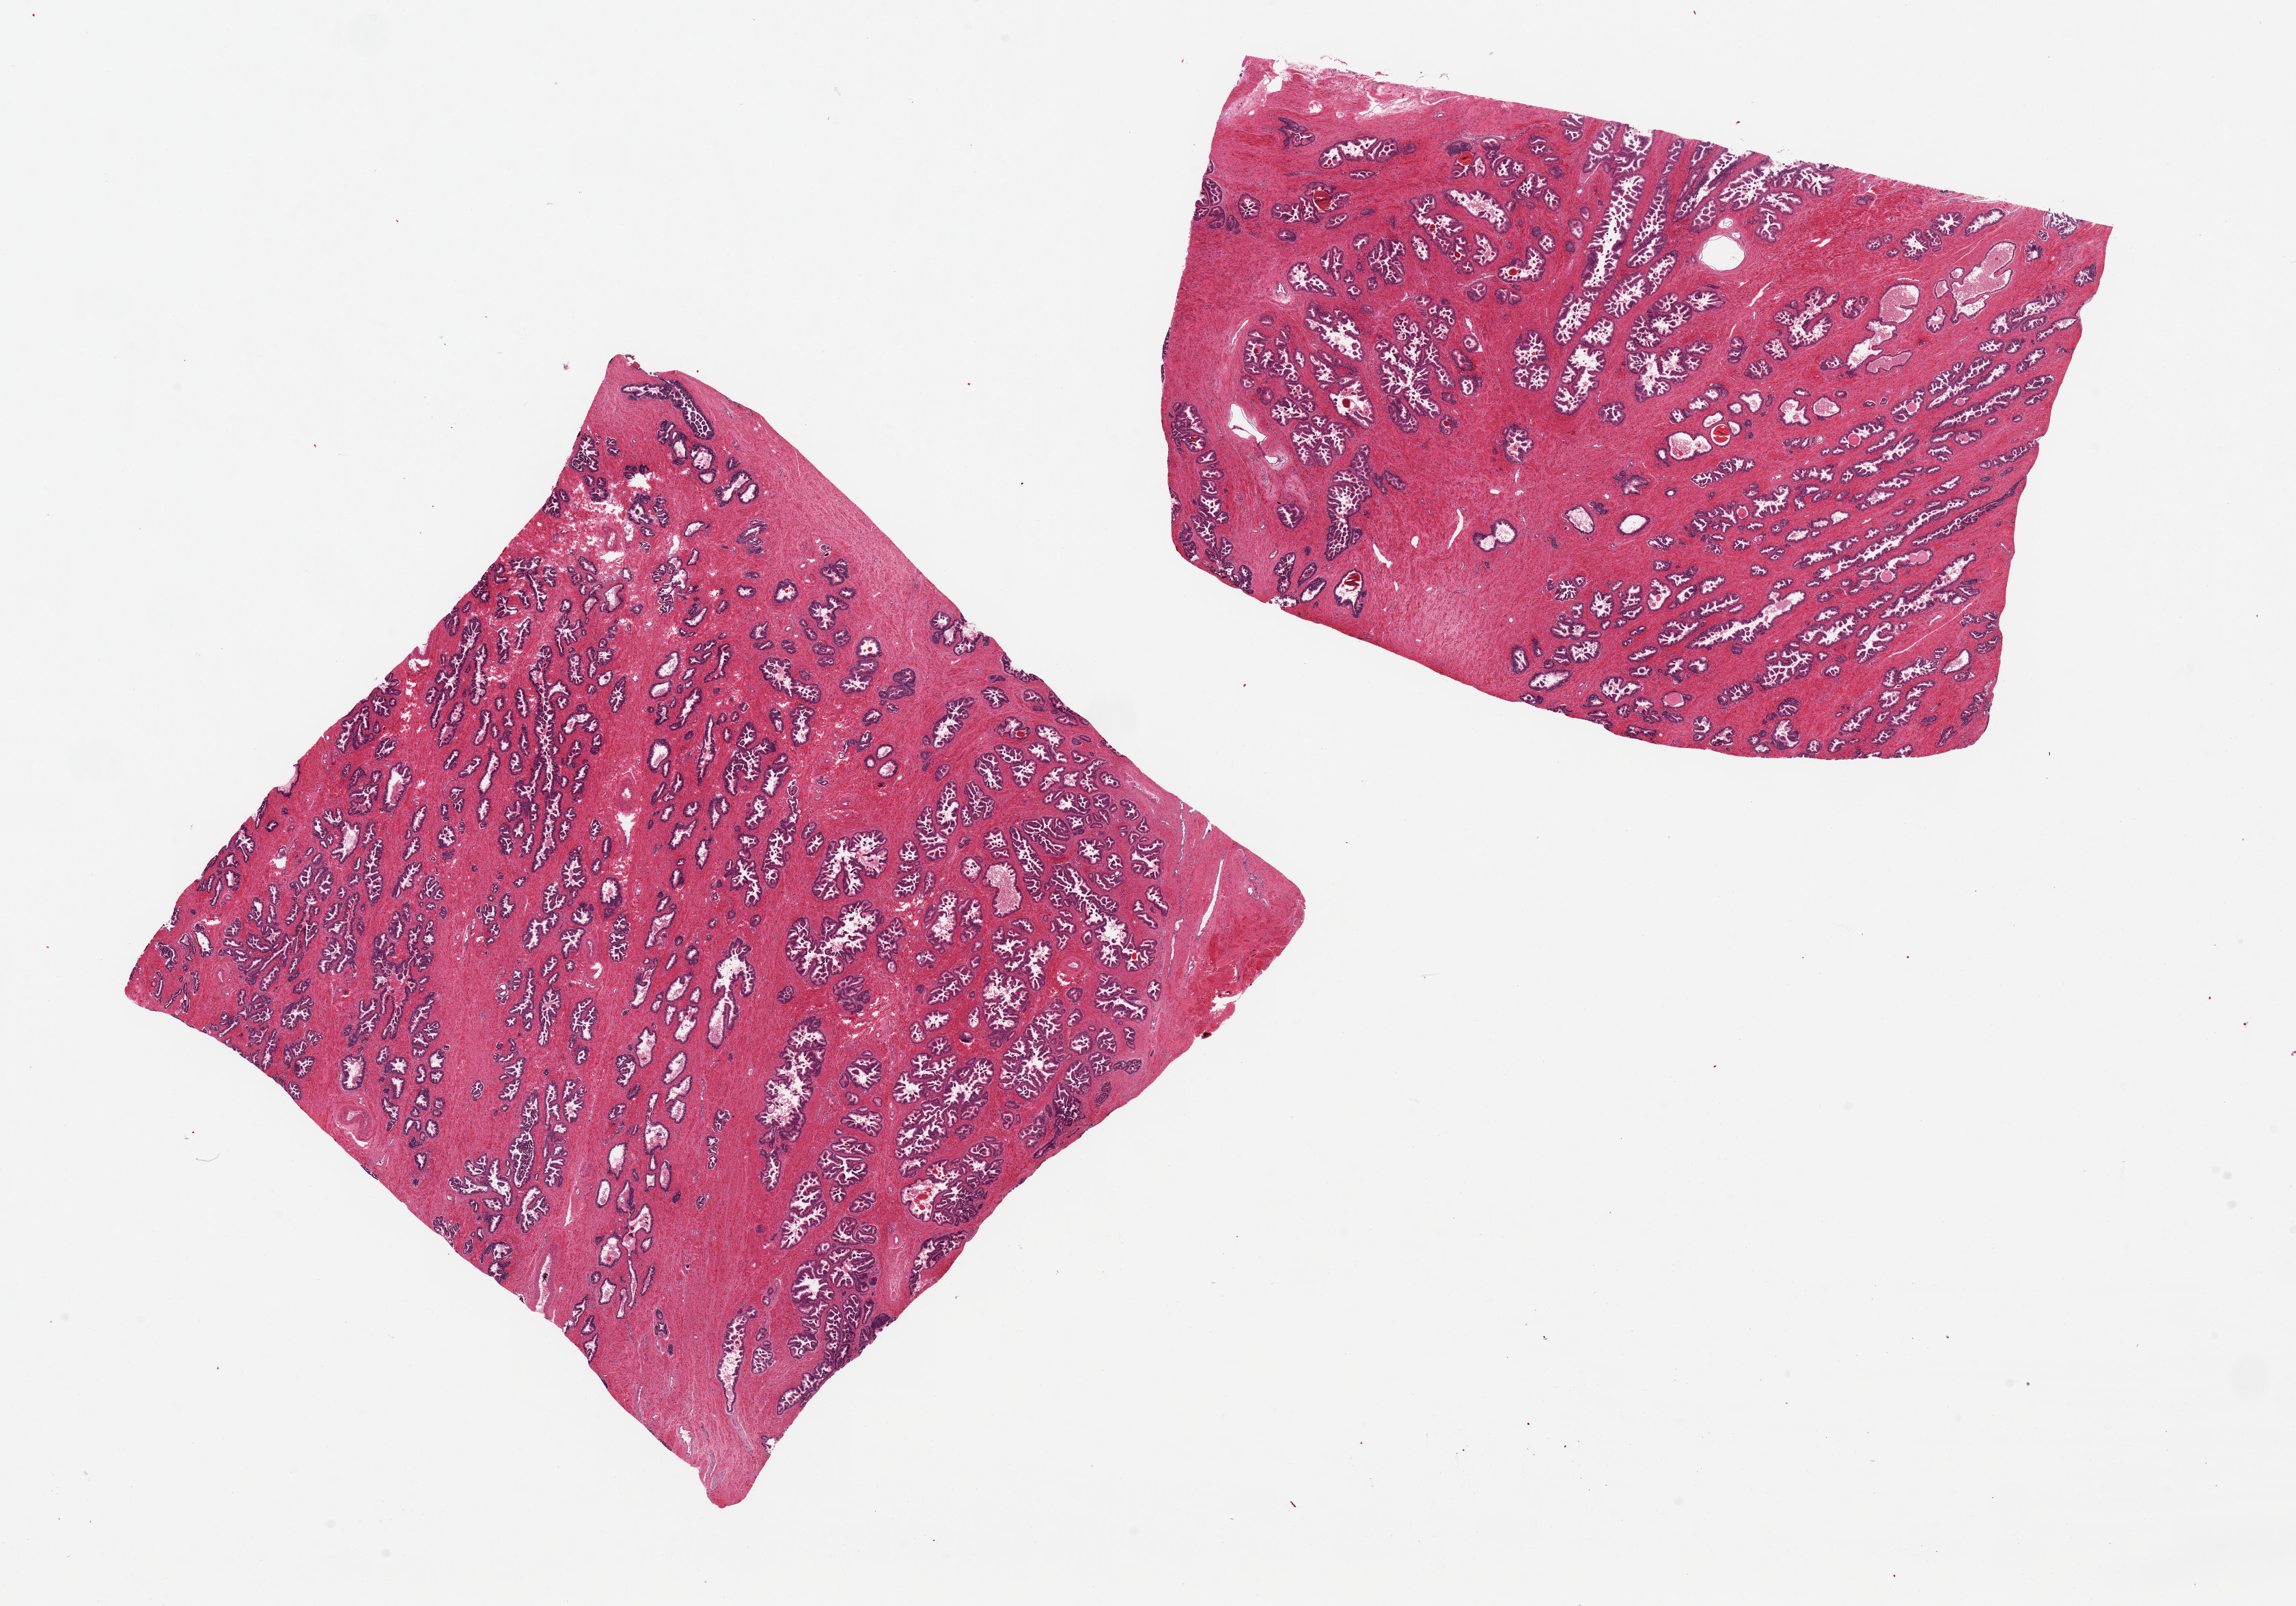
H&E whole-slide image, brightfield — a low-resolution overview of the entire scanned area, about 26.6 x 18.6 mm. PAXgene-fixed, paraffin-embedded tissue. Sampled site (target tissue): prostate. Tissue donor sample.
Review note (as recorded): 2 aliquots, ~10x8mm. Glandular epithelium remarkably well-preserved, prominent glandular hyperplasia.